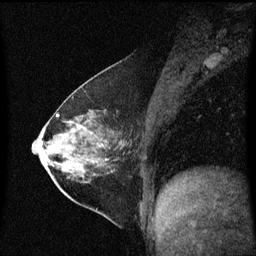
Breast MRI (dynamic contrast-enhanced), one sagittal slice; slice 25 of 60 in the series (ordered by position); dynamic contrast-enhanced series, image 2 of 3 at this slice position (ordered by acquisition); 1.5 T; TE 4.2 ms, TR 8.4 ms; 2 mm slice thickness; 256 × 256 image matrix, field of view 210 × 210 mm. Female patient, age 54 years. From the clinical record (not read from this slice): setting: breast cancer imaged before/during neoadjuvant chemotherapy; receptor status: HER2-positive.
Outlined on this slice (semi-automatic segmentation, software-assisted and operator-edited):
- analysis volume of interest (the breast-tissue region the enhancement analysis was run in; not a lesion): bounding box <59,115,128,199> (left, top, right, bottom; pixels)
- tumour enhancement mask (voxels above the 70 % enhancement threshold inside the analysis volume of interest): <100,145,104,147>